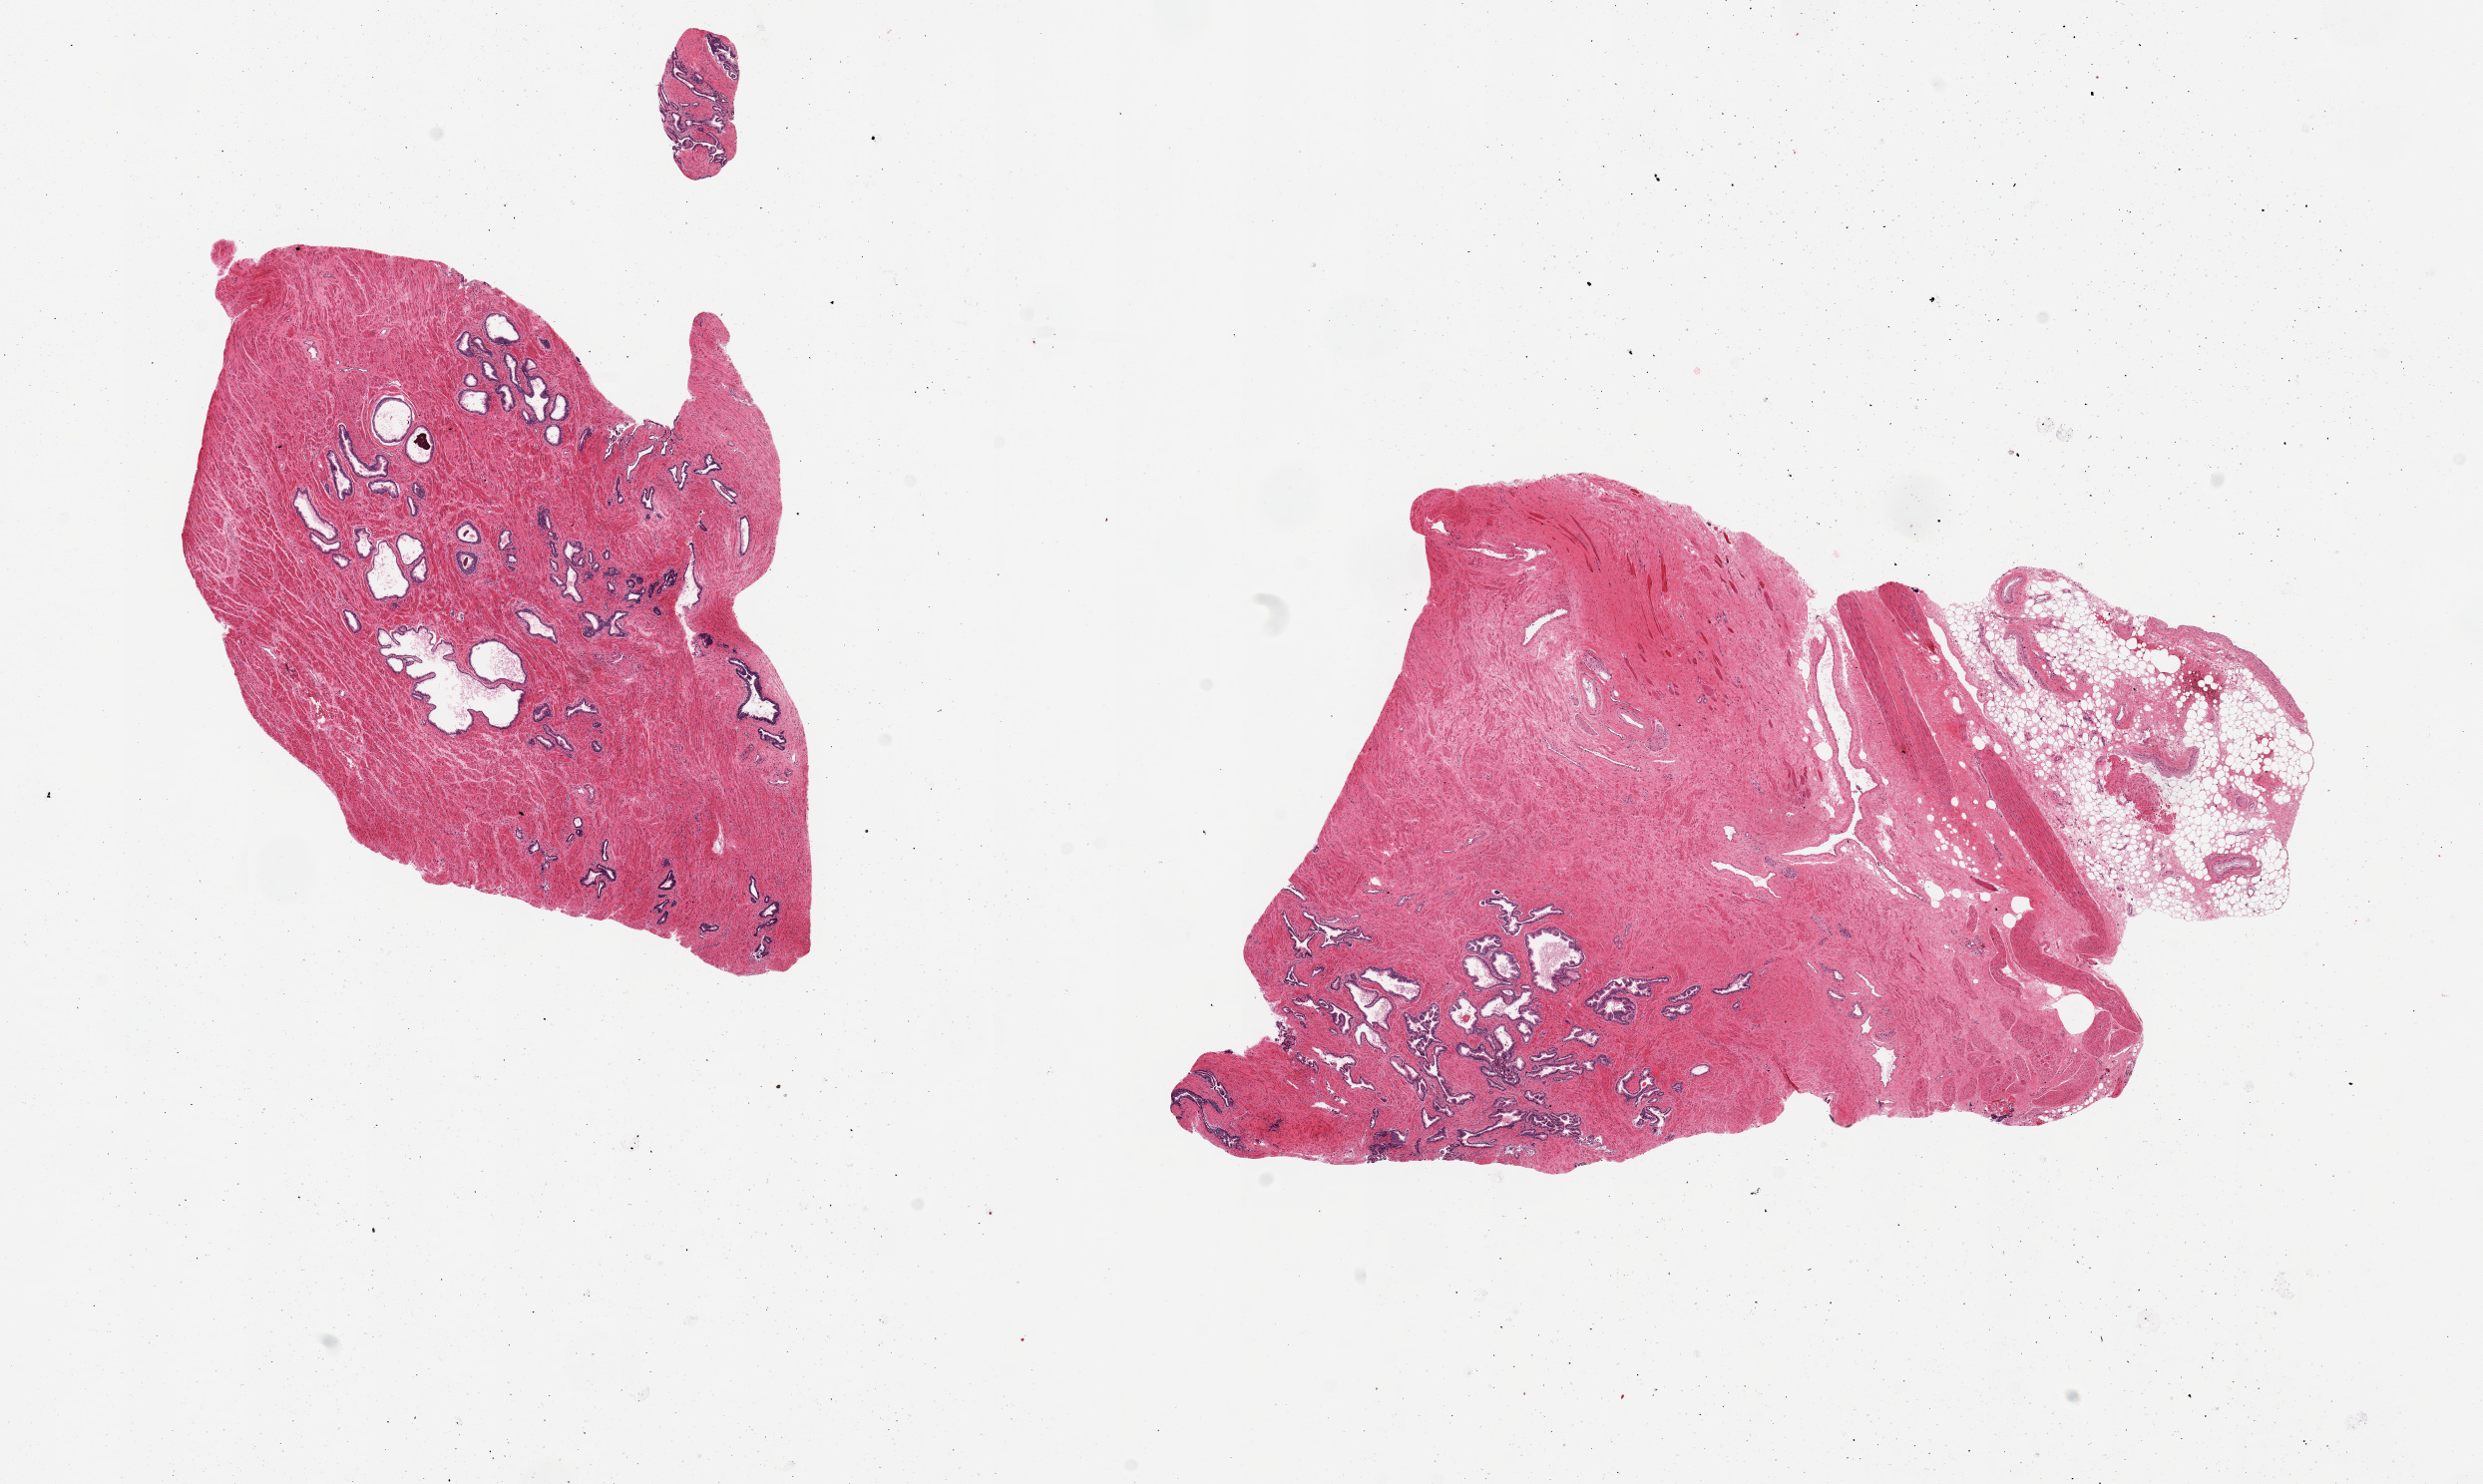
Digitized haematoxylin and eosin-stained section, shown as a low-resolution overview of the whole scanned area (about 19.7 x 11.8 mm). PAXgene-fixed paraffin-embedded (PFPE) section. Section of prostate (target tissue). Donor tissue sample. Male donor.
- review note (as recorded): 2 pieces